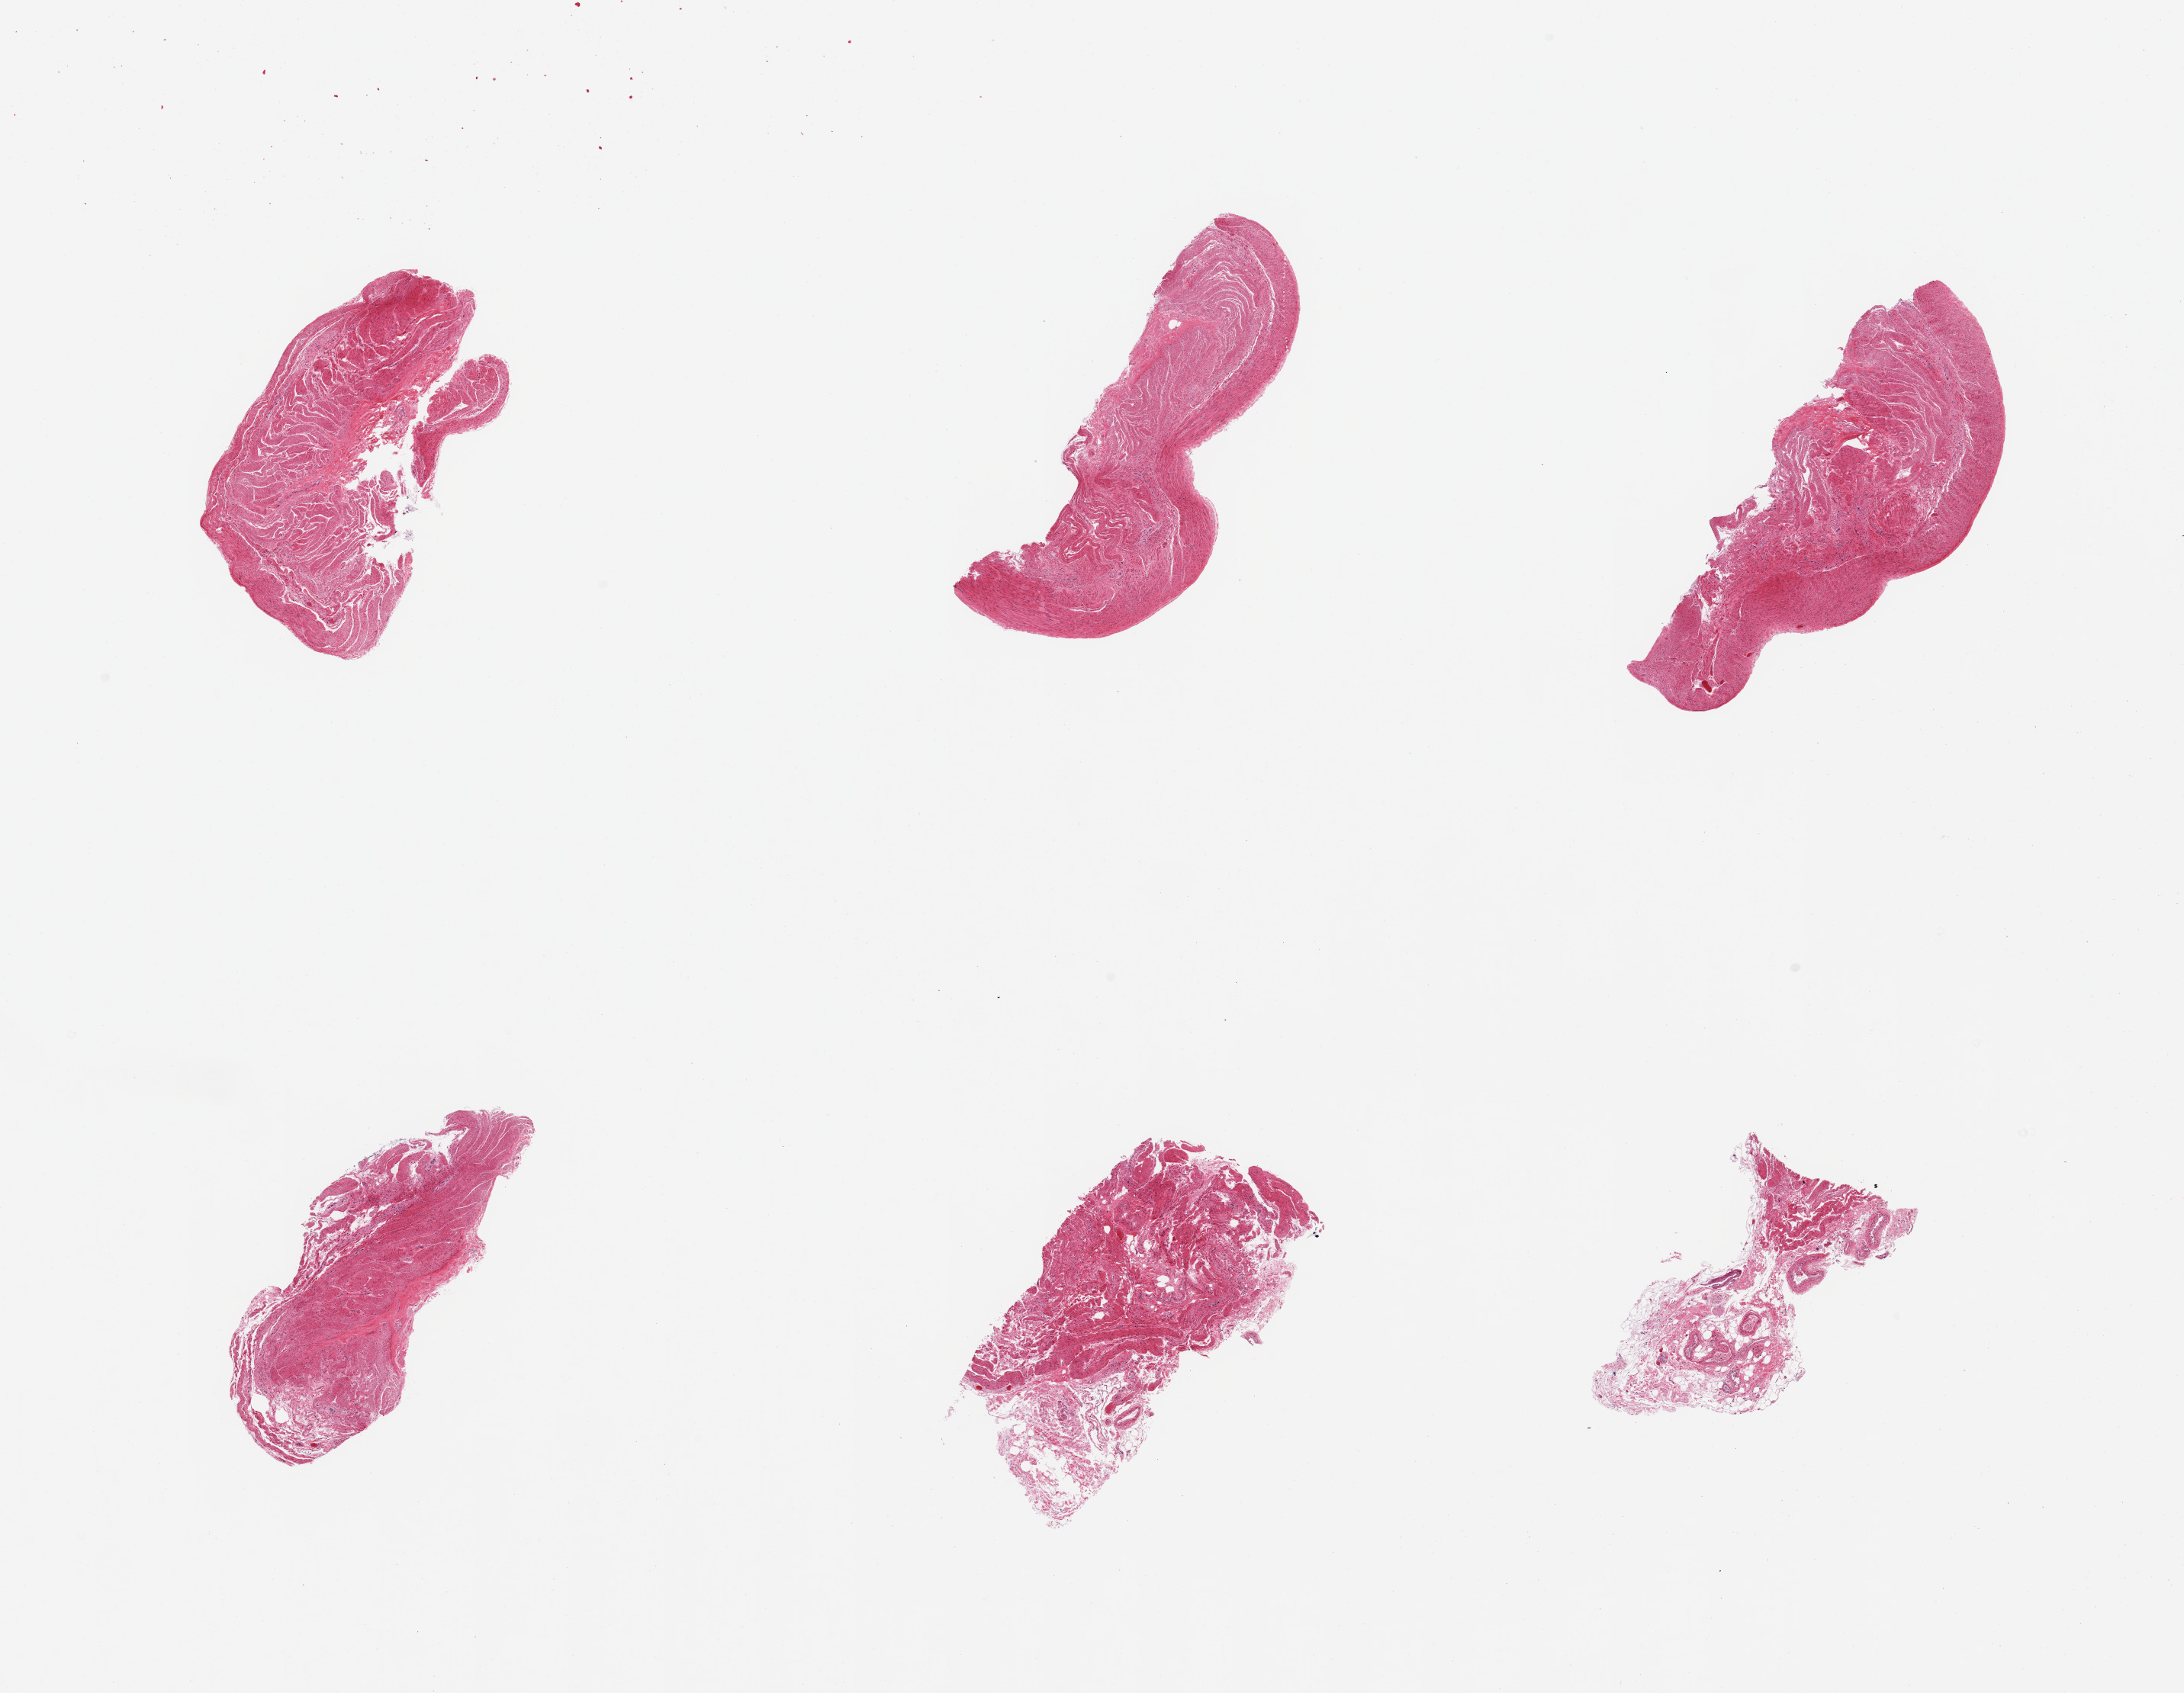
Whole-slide image, haematoxylin and eosin stain — low-resolution overview of the scanned area, about 22.6 x 17.6 mm. PAXgene-fixed, paraffin-embedded tissue. Section of ileum (target tissue). Donor tissue sample. Donor sex: male.
- review note (as recorded): 6 pieces; mostly muscularis and serosa; no evidence of mucosa or lymphoid aggregates